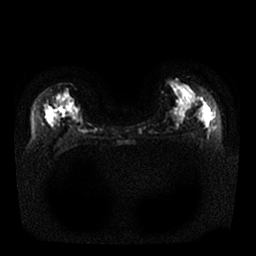
Breast MRI, one axial slice. Slice 15 of 25 in the series (ordered by position). Diffusion-weighted series; image 2 of 4 stored at this slice position (different b-values; order by instance number). 1.5 T. 4 mm slice thickness. 256 × 256 image matrix, field of view 340 × 340 mm. Female patient.
Outlined on this slice (manually delineated by an expert):
- tumour on diffusion-weighted imaging: box from (x=52, y=110) to (x=57, y=120) px